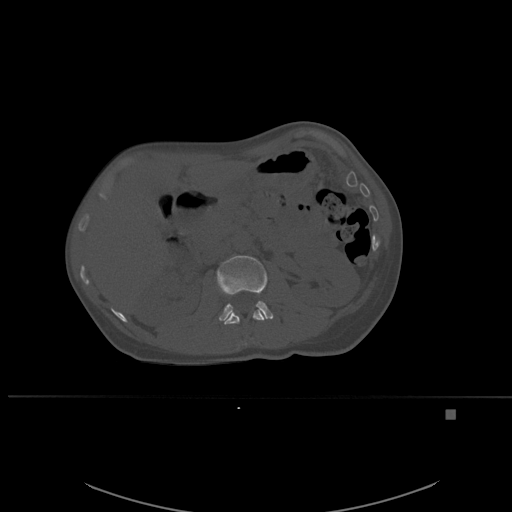
CT including the spine, one axial slice. Slice 246 of 537 in the series (ordered by position). Bone window (W 1800 / L 400 HU). 1.5 mm slice thickness. 512 × 512 image matrix, field of view 440 × 440 mm. Patient: female, 45 years. From the clinical record (not read from this slice): primary cancer: lung.
Annotated regions visible in this slice (semi-automatically segmented with operator editing):
- L1 vertebra: bounding box (x1, y1, x2, y2) in pixels: (224, 309, 266, 345)
- L2 vertebra: (217, 255, 274, 321)